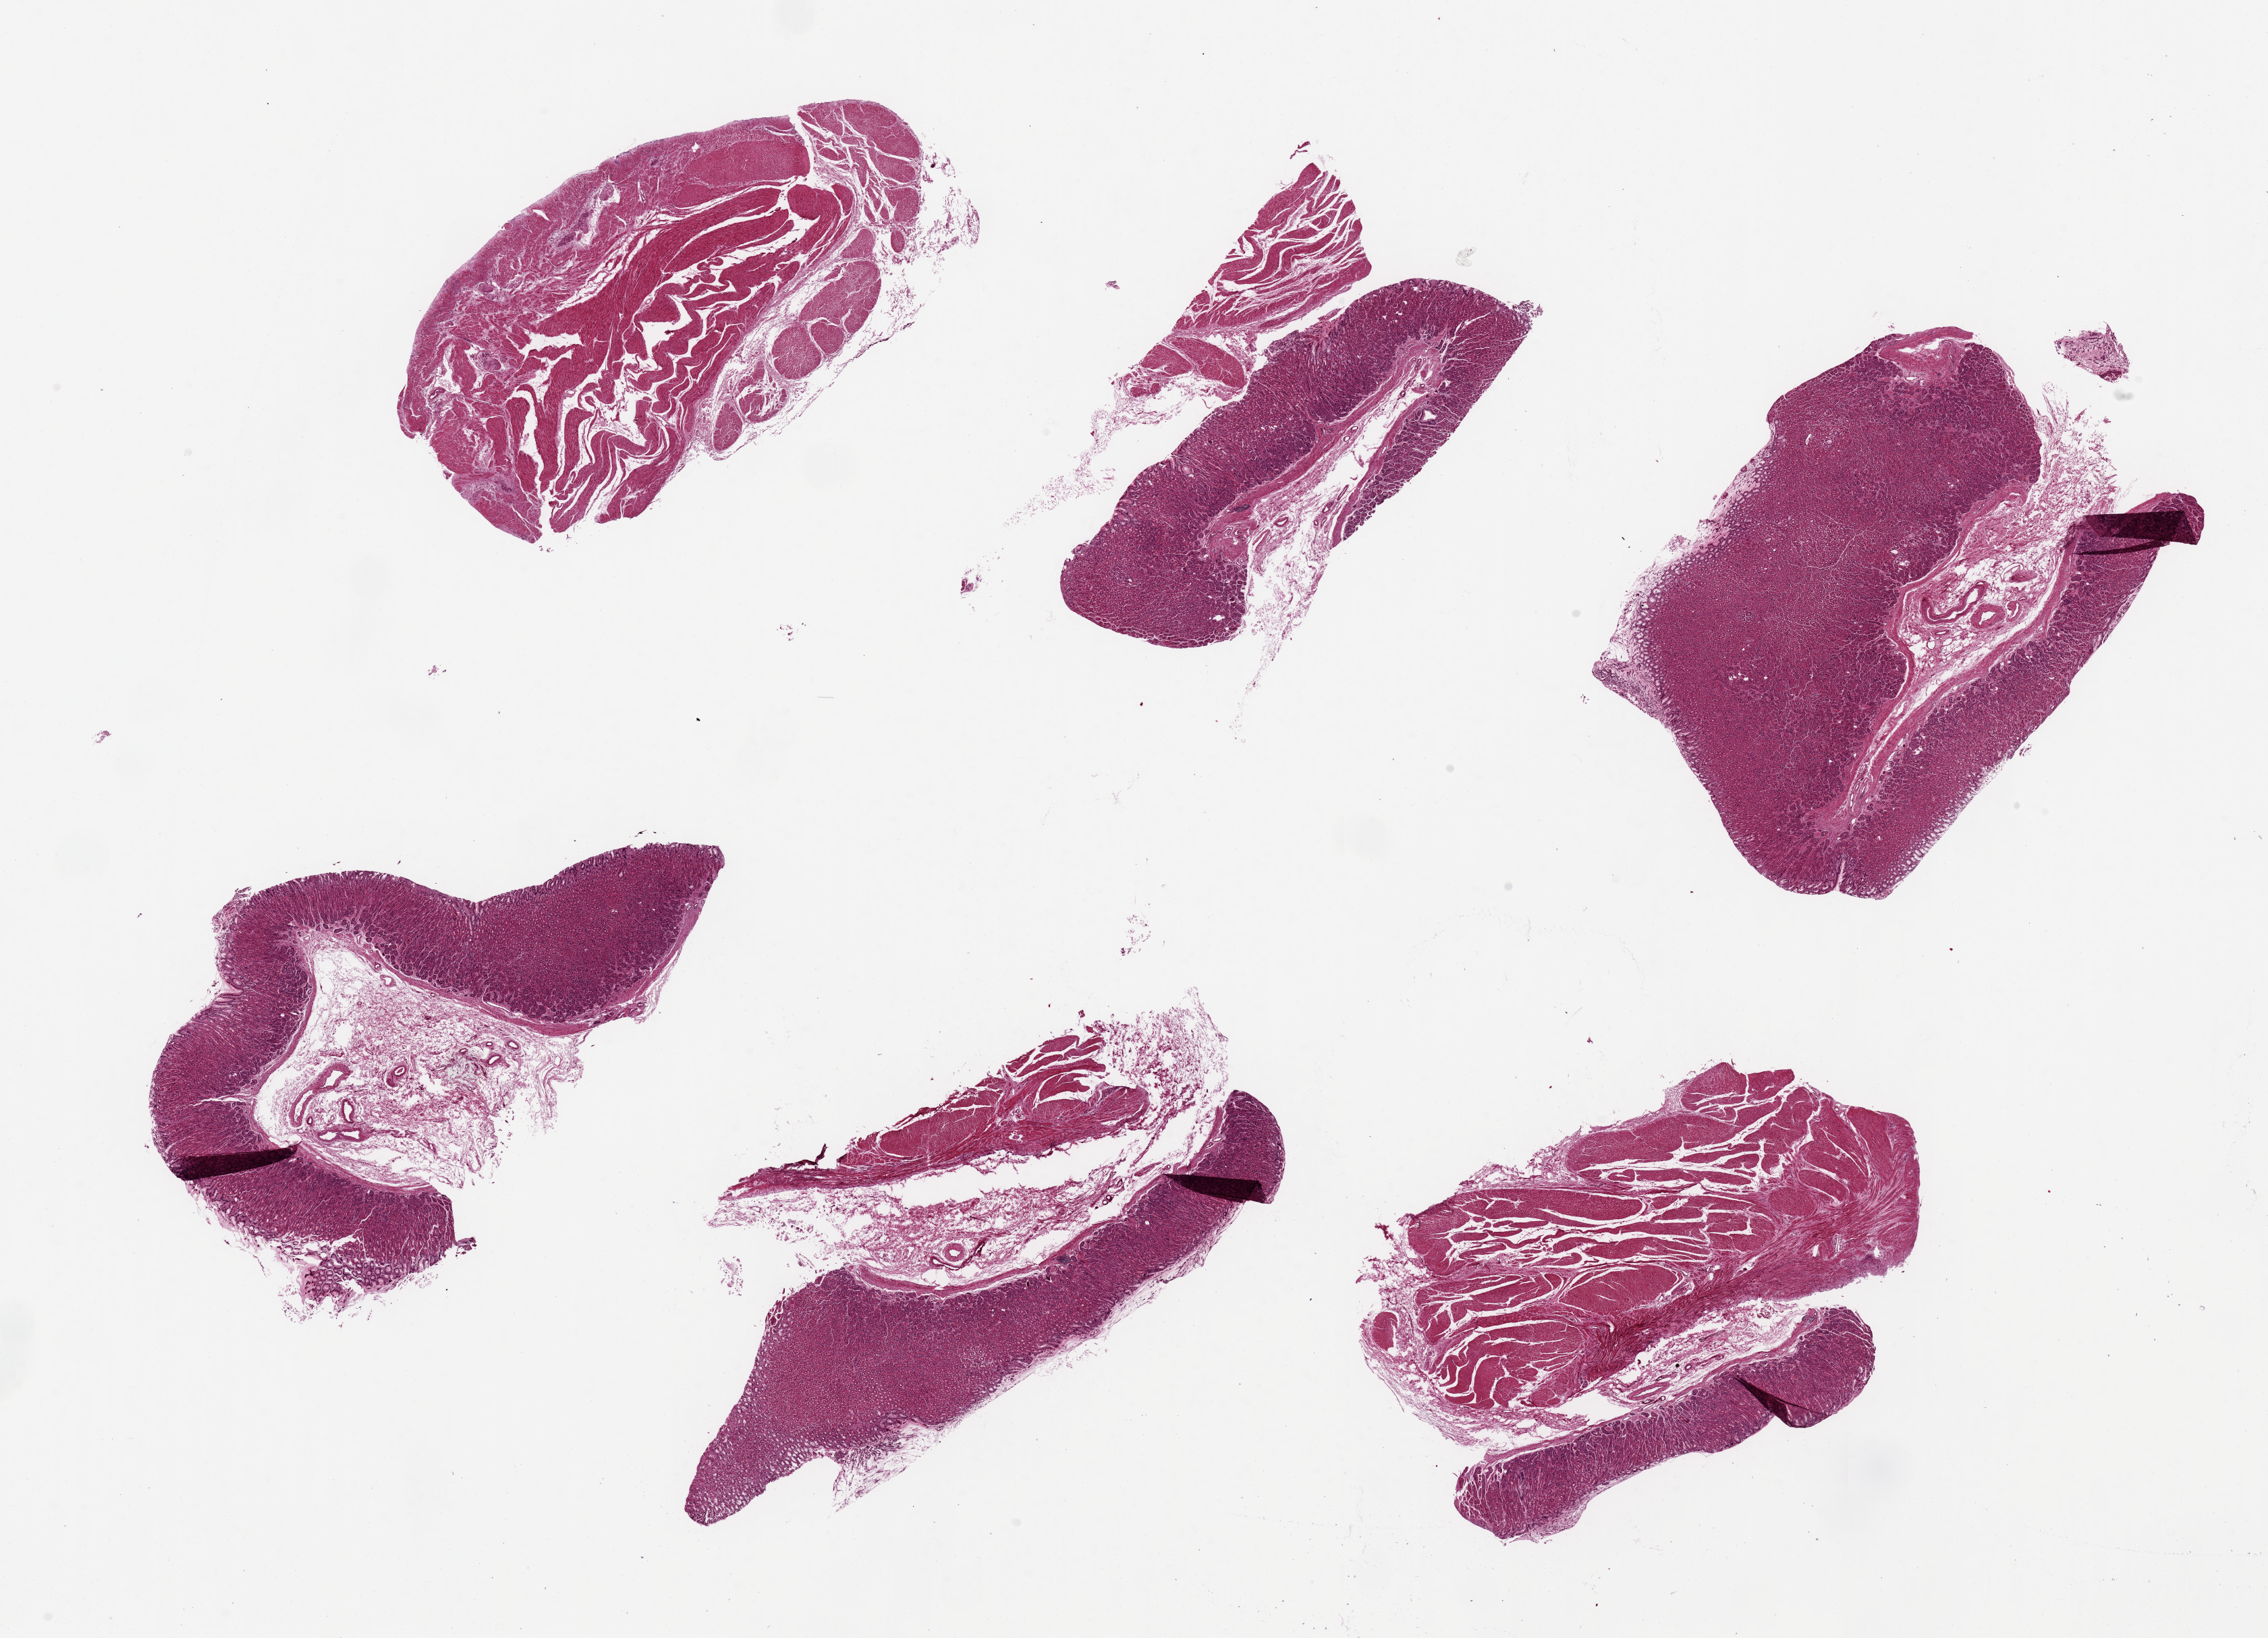
Whole-slide image, H&E stain — low-resolution overview of the scanned area, about 26.6 x 19.2 mm (acquisition: 20x scan), PAXgene-fixed, paraffin-embedded tissue, target tissue: stomach, donor tissue sample. Donor: male.
- review note (as recorded): 6 pieces up to 6x4 mm; 3 have mainly mucosa, 1 largely muscle